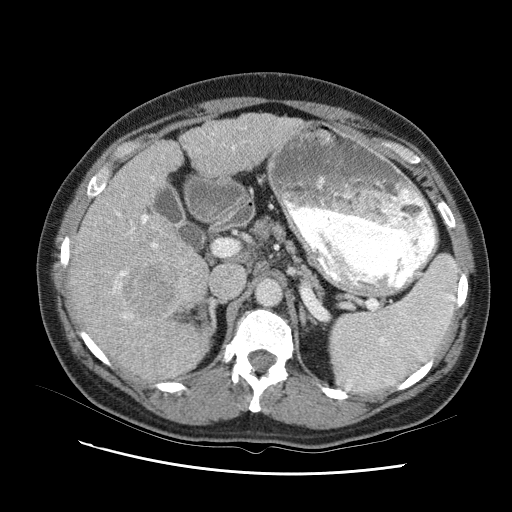
Contrast-enhanced abdominal CT (liver protocol), one axial slice. Position 56 of 95 along the scan axis. 120 kVp. One of 2 acquisitions stored at this slice position. Soft-tissue window (W 400 / L 40 HU). 2.5 mm slice thickness. 512 × 512 image matrix, field of view 360 × 360 mm. Case-level facts recorded for this patient, not image findings: diagnosis: hepatocellular carcinoma (patient treated with transarterial chemoembolisation; whether this scan precedes or follows treatment is not stated here); TNM stage (as recorded): Stage-I; Child-Pugh class: B; tumour nodularity: uninodular.
Structures marked on this image (semi-automatic segmentation, software-assisted and operator-edited):
- liver parenchyma outside the tumour (the mass and vessels are separate outlines, so this box may not span the whole liver): bounding box <68,108,309,380> (left, top, right, bottom; pixels)
- mass: <124,261,173,308>
- liver vessels: <92,137,237,369>